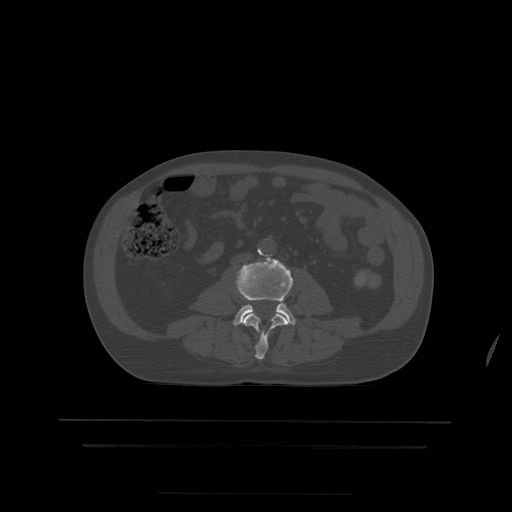
CT including the spine, one axial slice; position 107 of 522 along the scan axis; bone window (W 1800 / L 400 HU); 1.25 mm slice thickness; 512 × 512 image matrix, field of view 436 × 436 mm. Patient age 68 years. Case-level facts recorded for this patient, not image findings: primary cancer: urothelial.
Structures marked on this image (semi-automatic segmentation, software-assisted and operator-edited):
- L3 vertebra: box from (x=242, y=313) to (x=290, y=360) px
- L4 vertebra: (x=233, y=258)–(x=296, y=326)